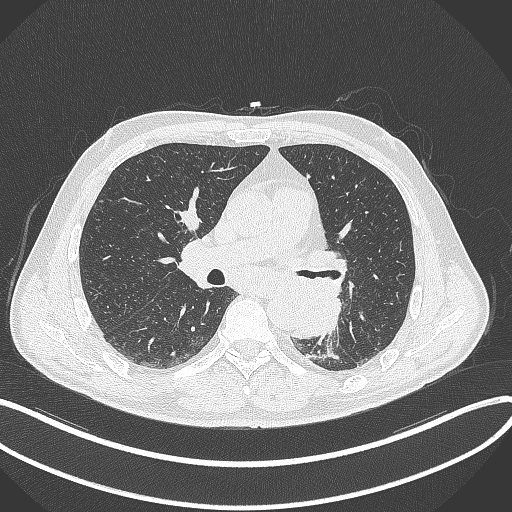
Chest CT, one axial slice; position 187 of 329 along the scan axis; reconstruction kernel B70f; 120 kVp; lung window (W 1500 / L -600 HU); 512 × 512 image matrix, field of view 400 × 400 mm. Patient: male, 59 years. From the clinical record (not read from this slice): clinical TNM (as recorded): T2a N2 M0.
Outlined on this slice (bounding box drawn by a radiologist):
- lung tumour (recorded histology: squamous cell carcinoma): bounding box [x1, y1, x2, y2] px = [286, 275, 345, 343]